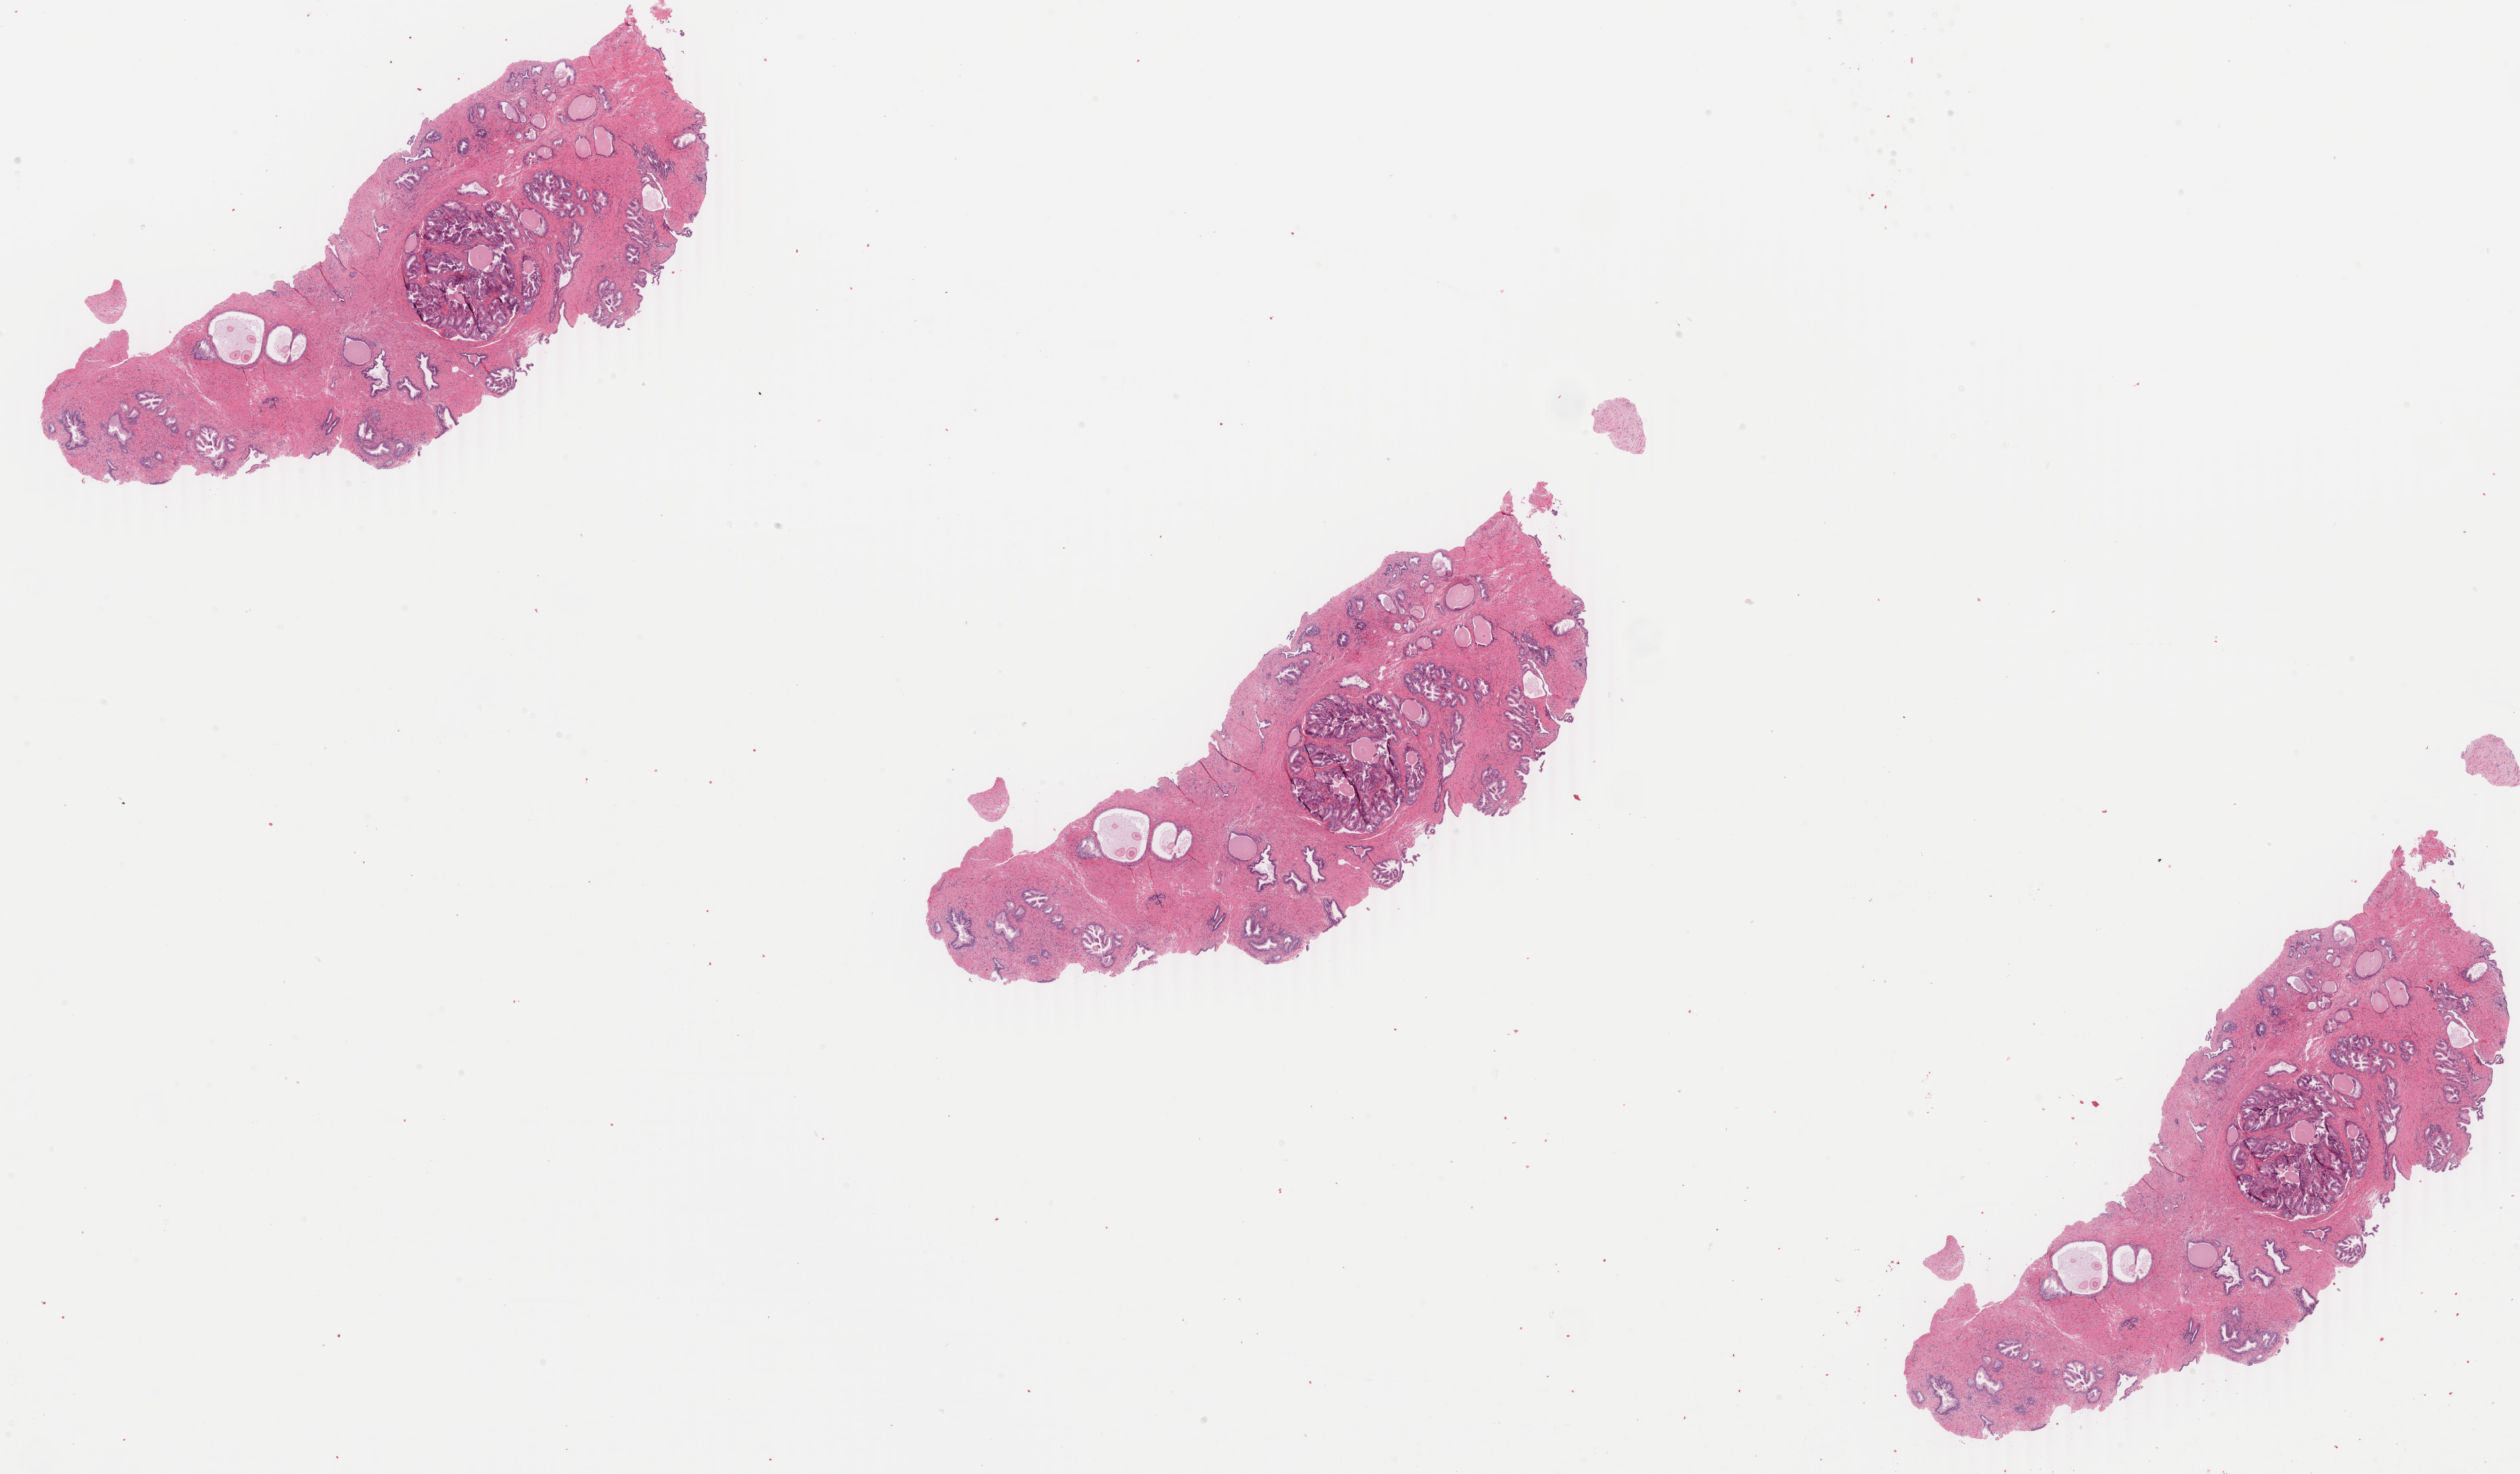
Whole-slide histology image, Hematoxylin and eosin (H&E) stained, low-resolution overview of the scanned area, about 30.2 x 17.7 mm. Formalin-fixed paraffin-embedded (FFPE) diagnostic section. Primary tumour sample from the prostate. Male, age 60 years at initial diagnosis. Gleason score: 6 (3+3).
Laterality: bilateral. Pathologic diagnosis: Adenocarcinoma, NOS (prostate gland).